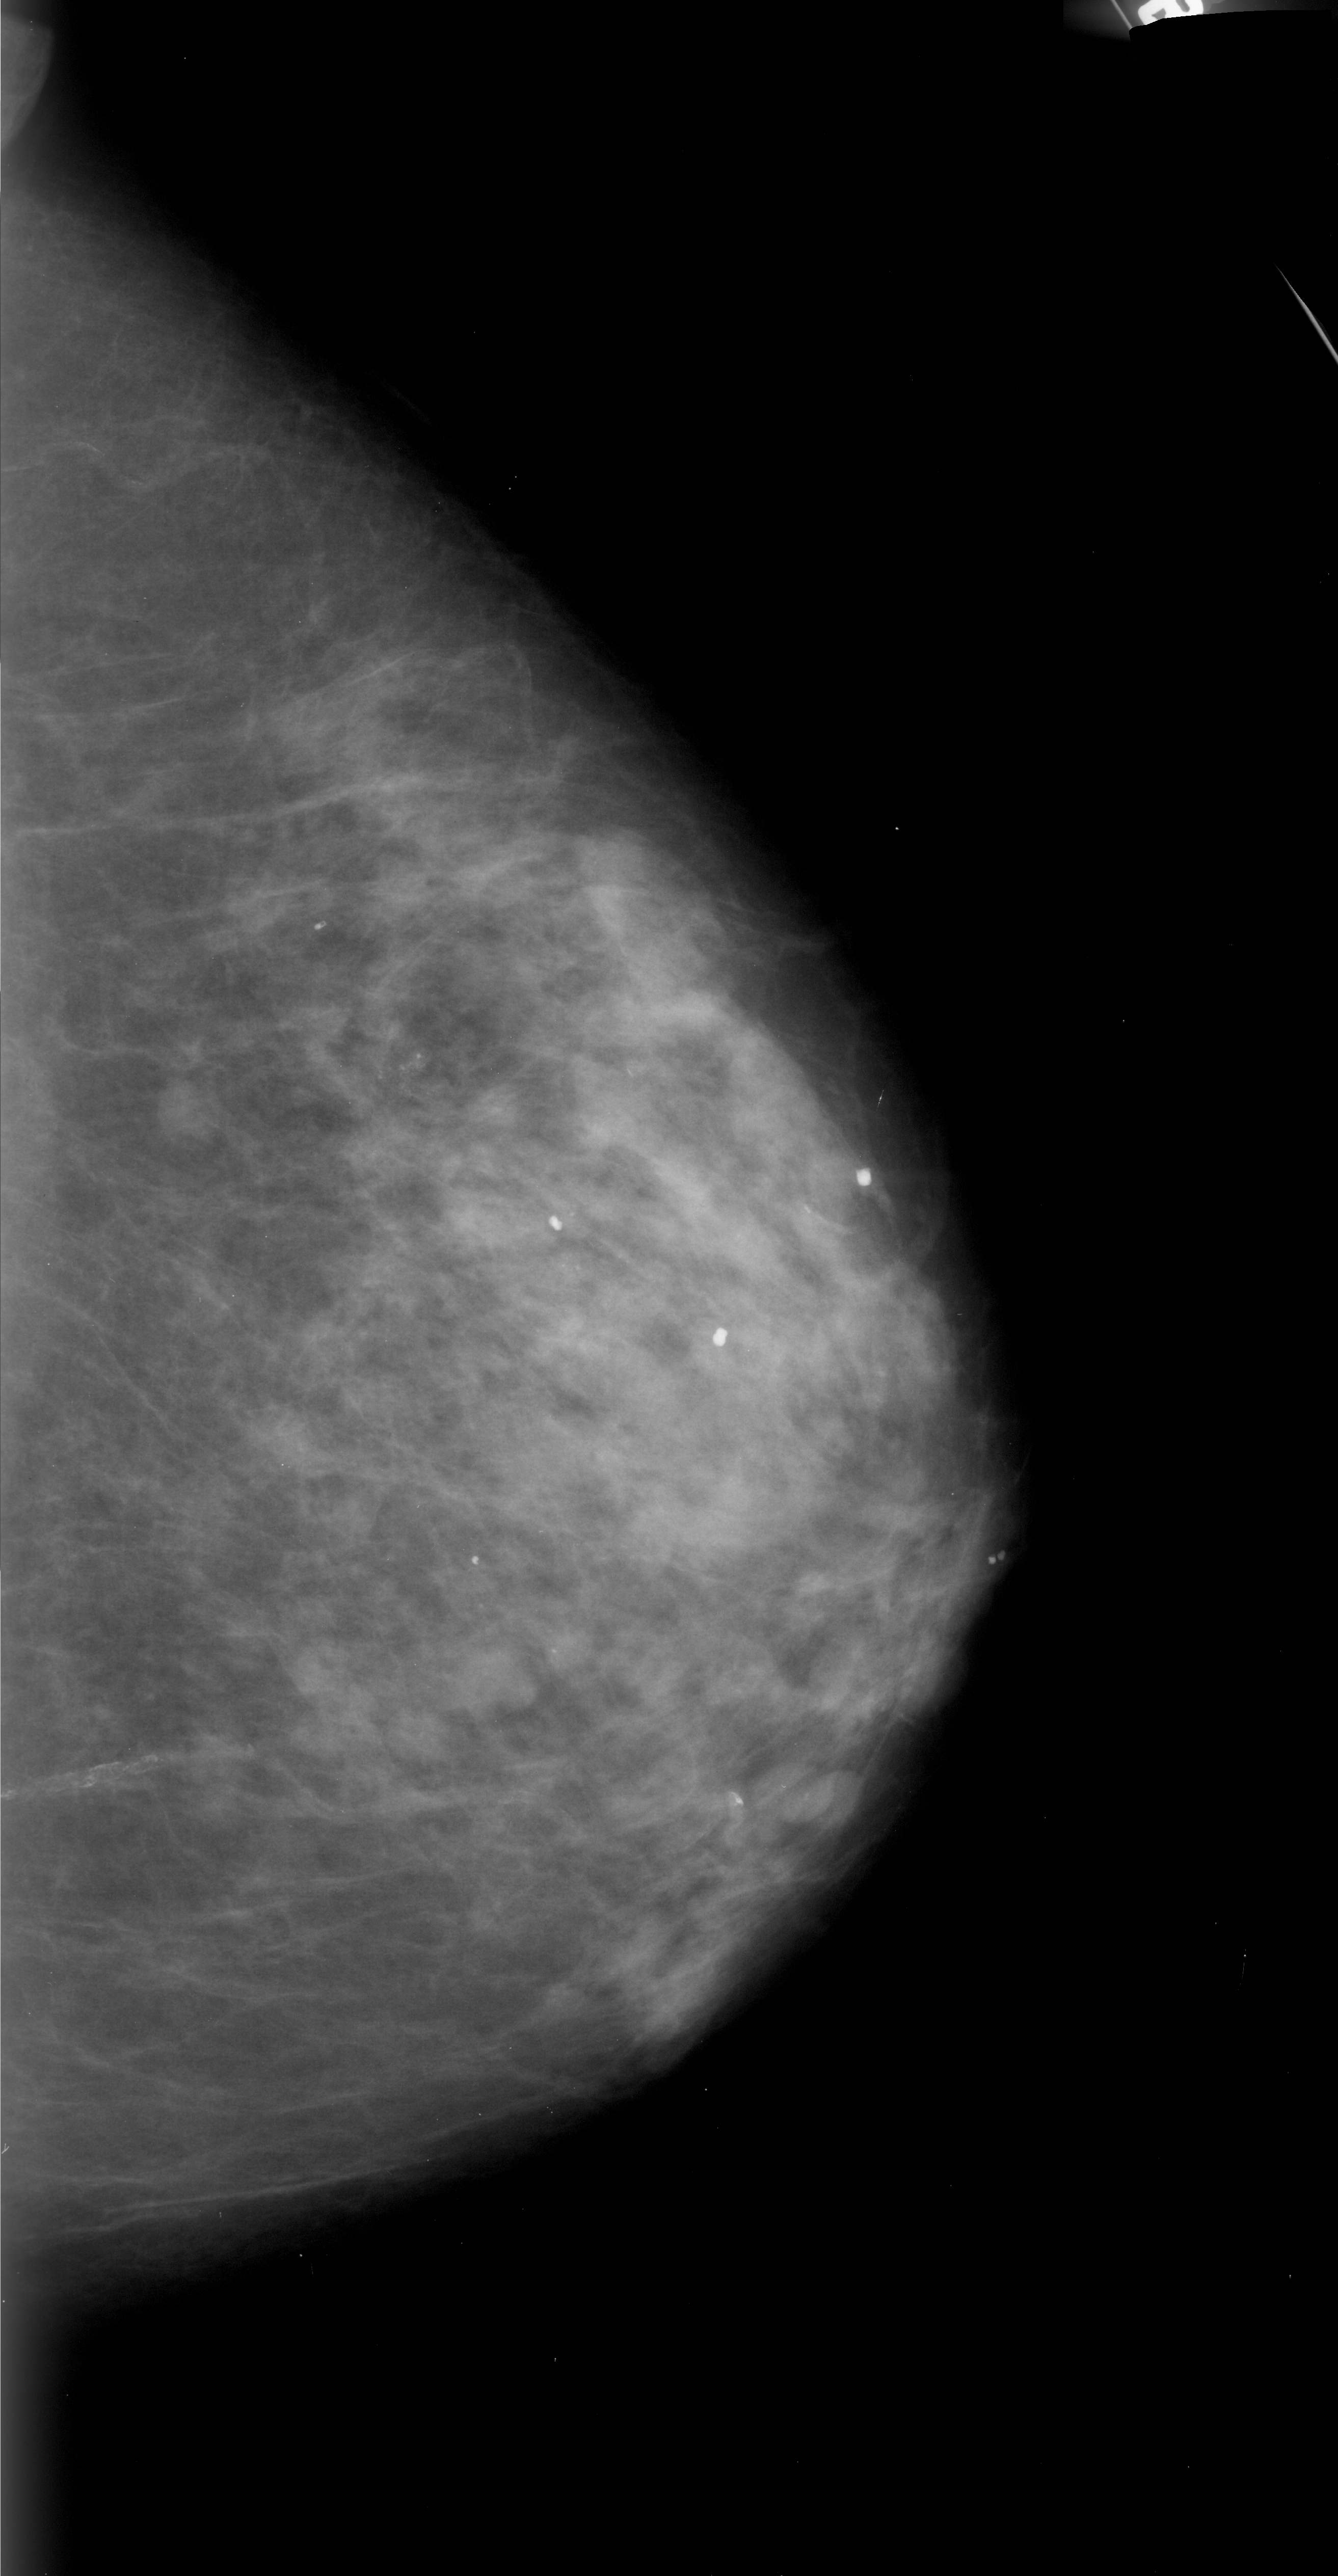
Digitized screen-film mammogram, right breast, CC view, breast composition: heterogeneously dense (BI-RADS density category 3 of 4).
- Marked abnormality: calcifications, morphology pleomorphic, distribution clustered; BI-RADS assessment category 4; subtlety rating 2 on a 1 (subtle) to 5 (obvious) scale; pathology (as recorded): malignant.